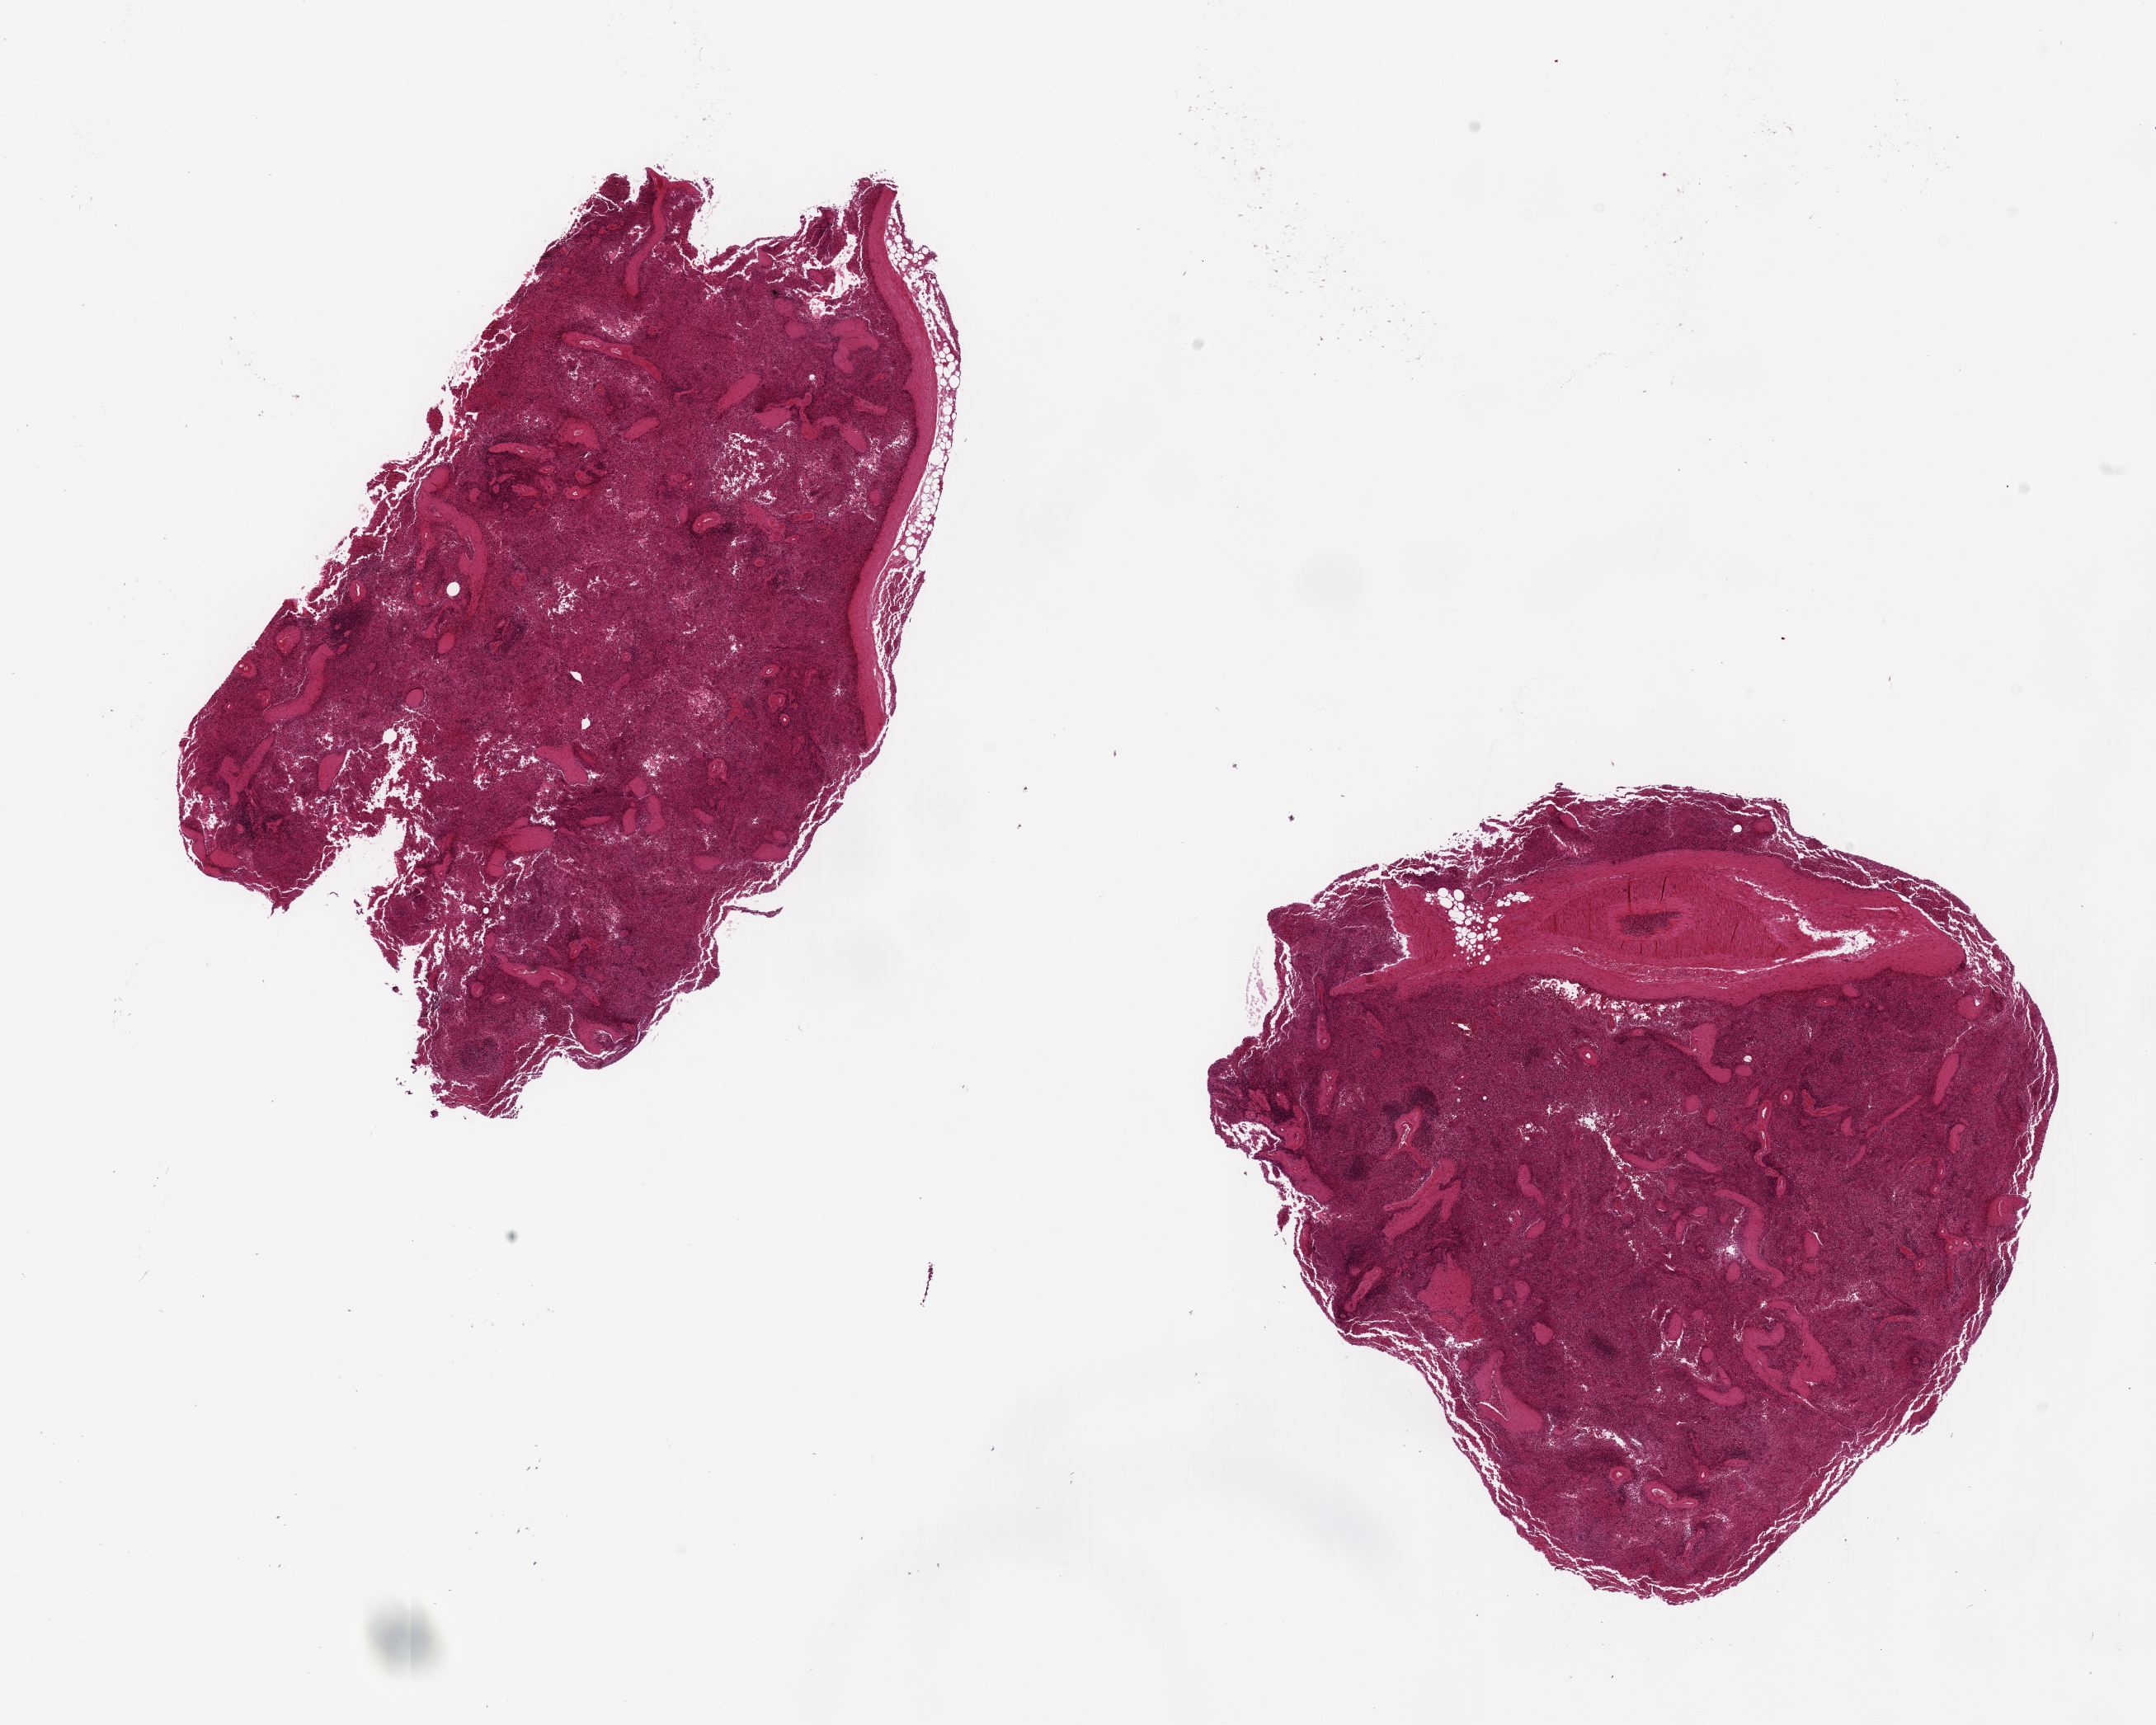
Haematoxylin and eosin whole-slide image — low-resolution overview of the scanned area, about 20.7 x 16.5 mm; PAXgene-fixed, paraffin-embedded tissue; section of spleen (target tissue); donor tissue sample. Donor: female.
Review note (as recorded): 2 pieces, 8x7 & 9x5mm; moderately congested; capsule on one edge.